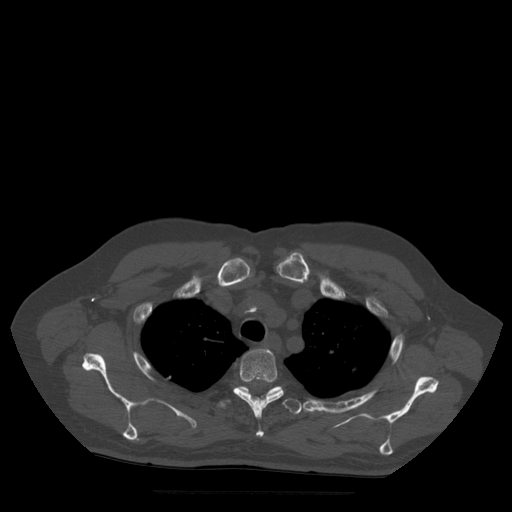
CT including the spine, one axial slice; slice 405 of 522 in the series (ordered by position); bone window (W 1800 / L 400 HU); 1.25 mm slice thickness; 512 × 512 image matrix. Patient age 72 years. Case-level facts recorded for this patient, not image findings: primary cancer: prostate.
Outlined on this slice (semi-automatically segmented with operator editing):
- T3 vertebra: bounding box <233,349,284,437> (left, top, right, bottom; pixels)
- T4 vertebra: <218,387,304,415>